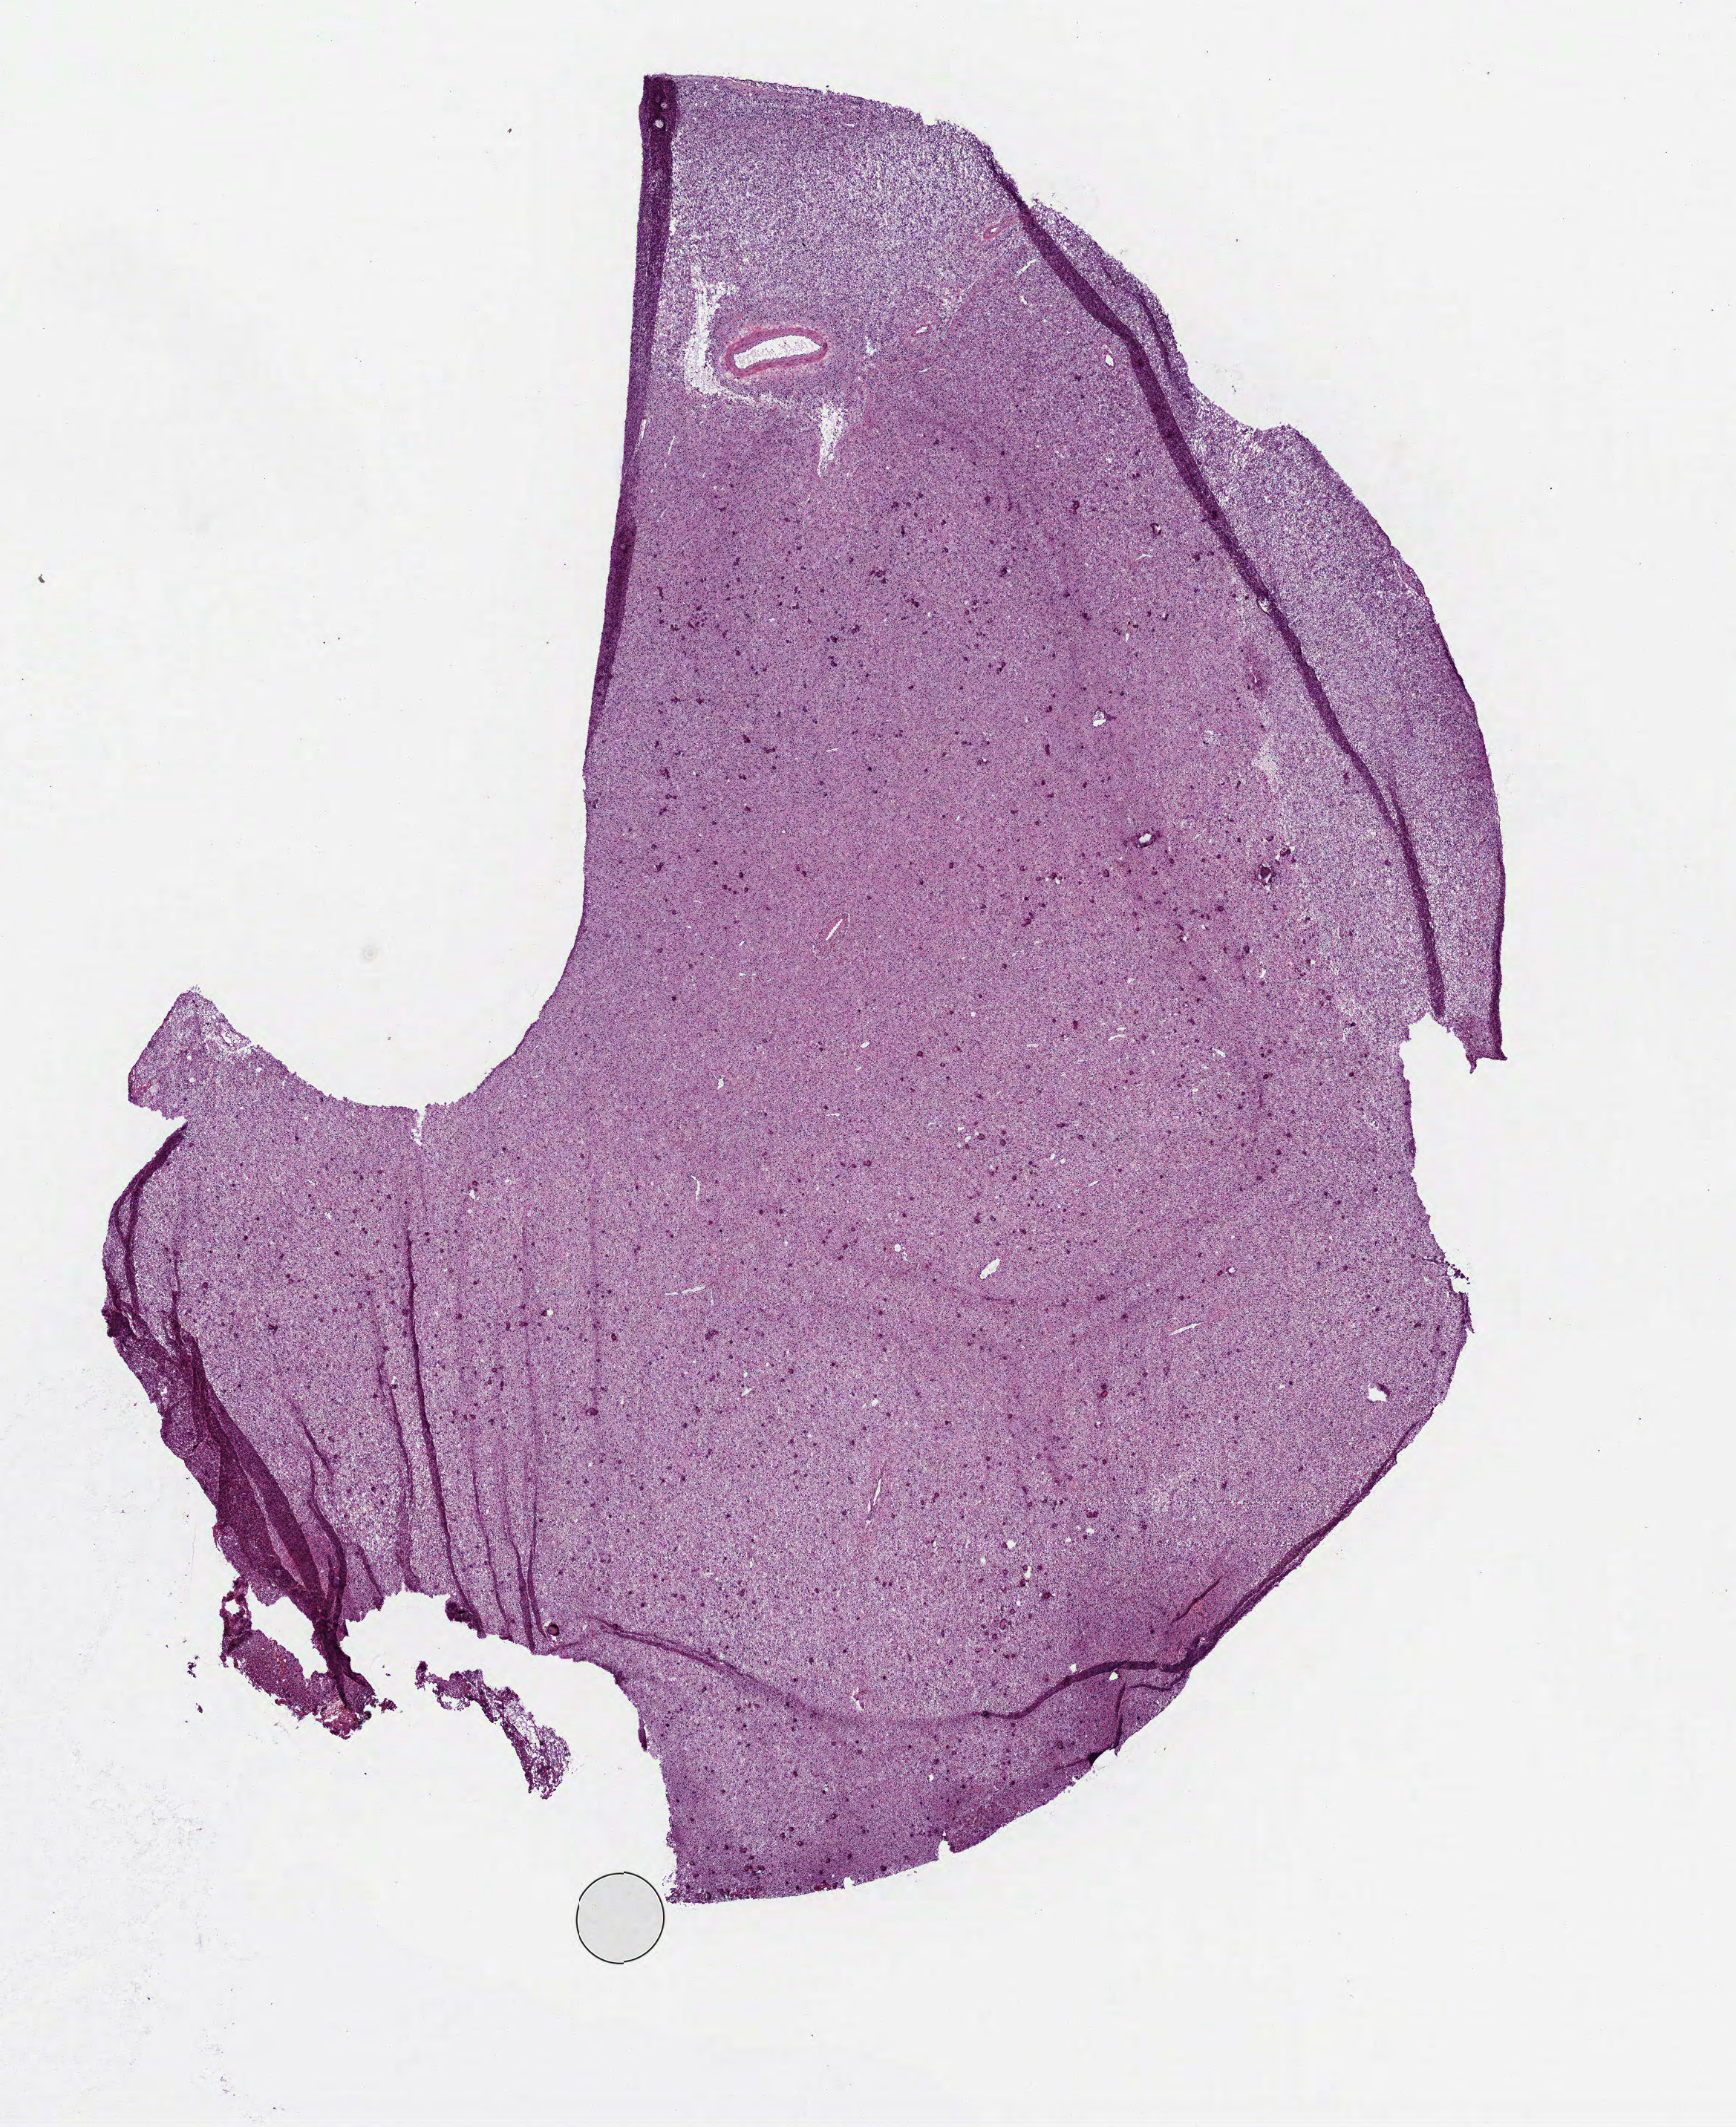
Digitized Hematoxylin and eosin (H&E) stained tissue section (whole slide) — whole scanned area (about 9.4 x 11.6 mm, from a 40x scan) shown as a low-resolution overview; frozen section; brain, primary tumour sample. Female, age 60 years at initial diagnosis.
Pathologic diagnosis: Astrocytoma, anaplastic (cerebrum).